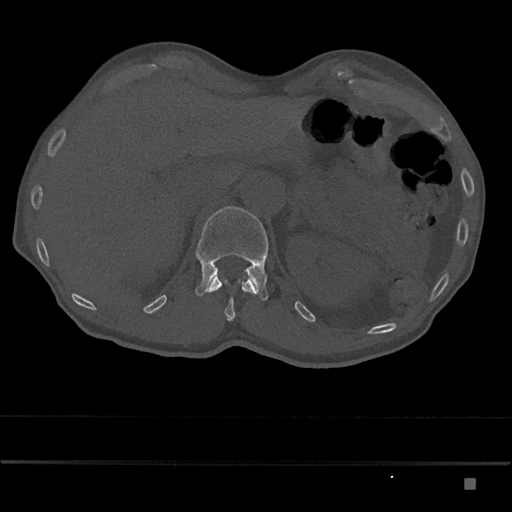
CT including the spine, one axial slice; slice 574 of 797 in the series (ordered by position); reconstruction kernel Br40s/3; bone window (W 1800 / L 400 HU); 512 × 512 image matrix, field of view 390 × 390 mm. Patient: male, 72 years. Case-level facts recorded for this patient, not image findings: primary cancer: prostate.
Outlined on this slice (semi-automatic segmentation, software-assisted and operator-edited):
- L1 vertebra: bounding box (x1, y1, x2, y2) in pixels: (195, 206, 269, 301)
- T12 vertebra: (205, 276, 256, 321)